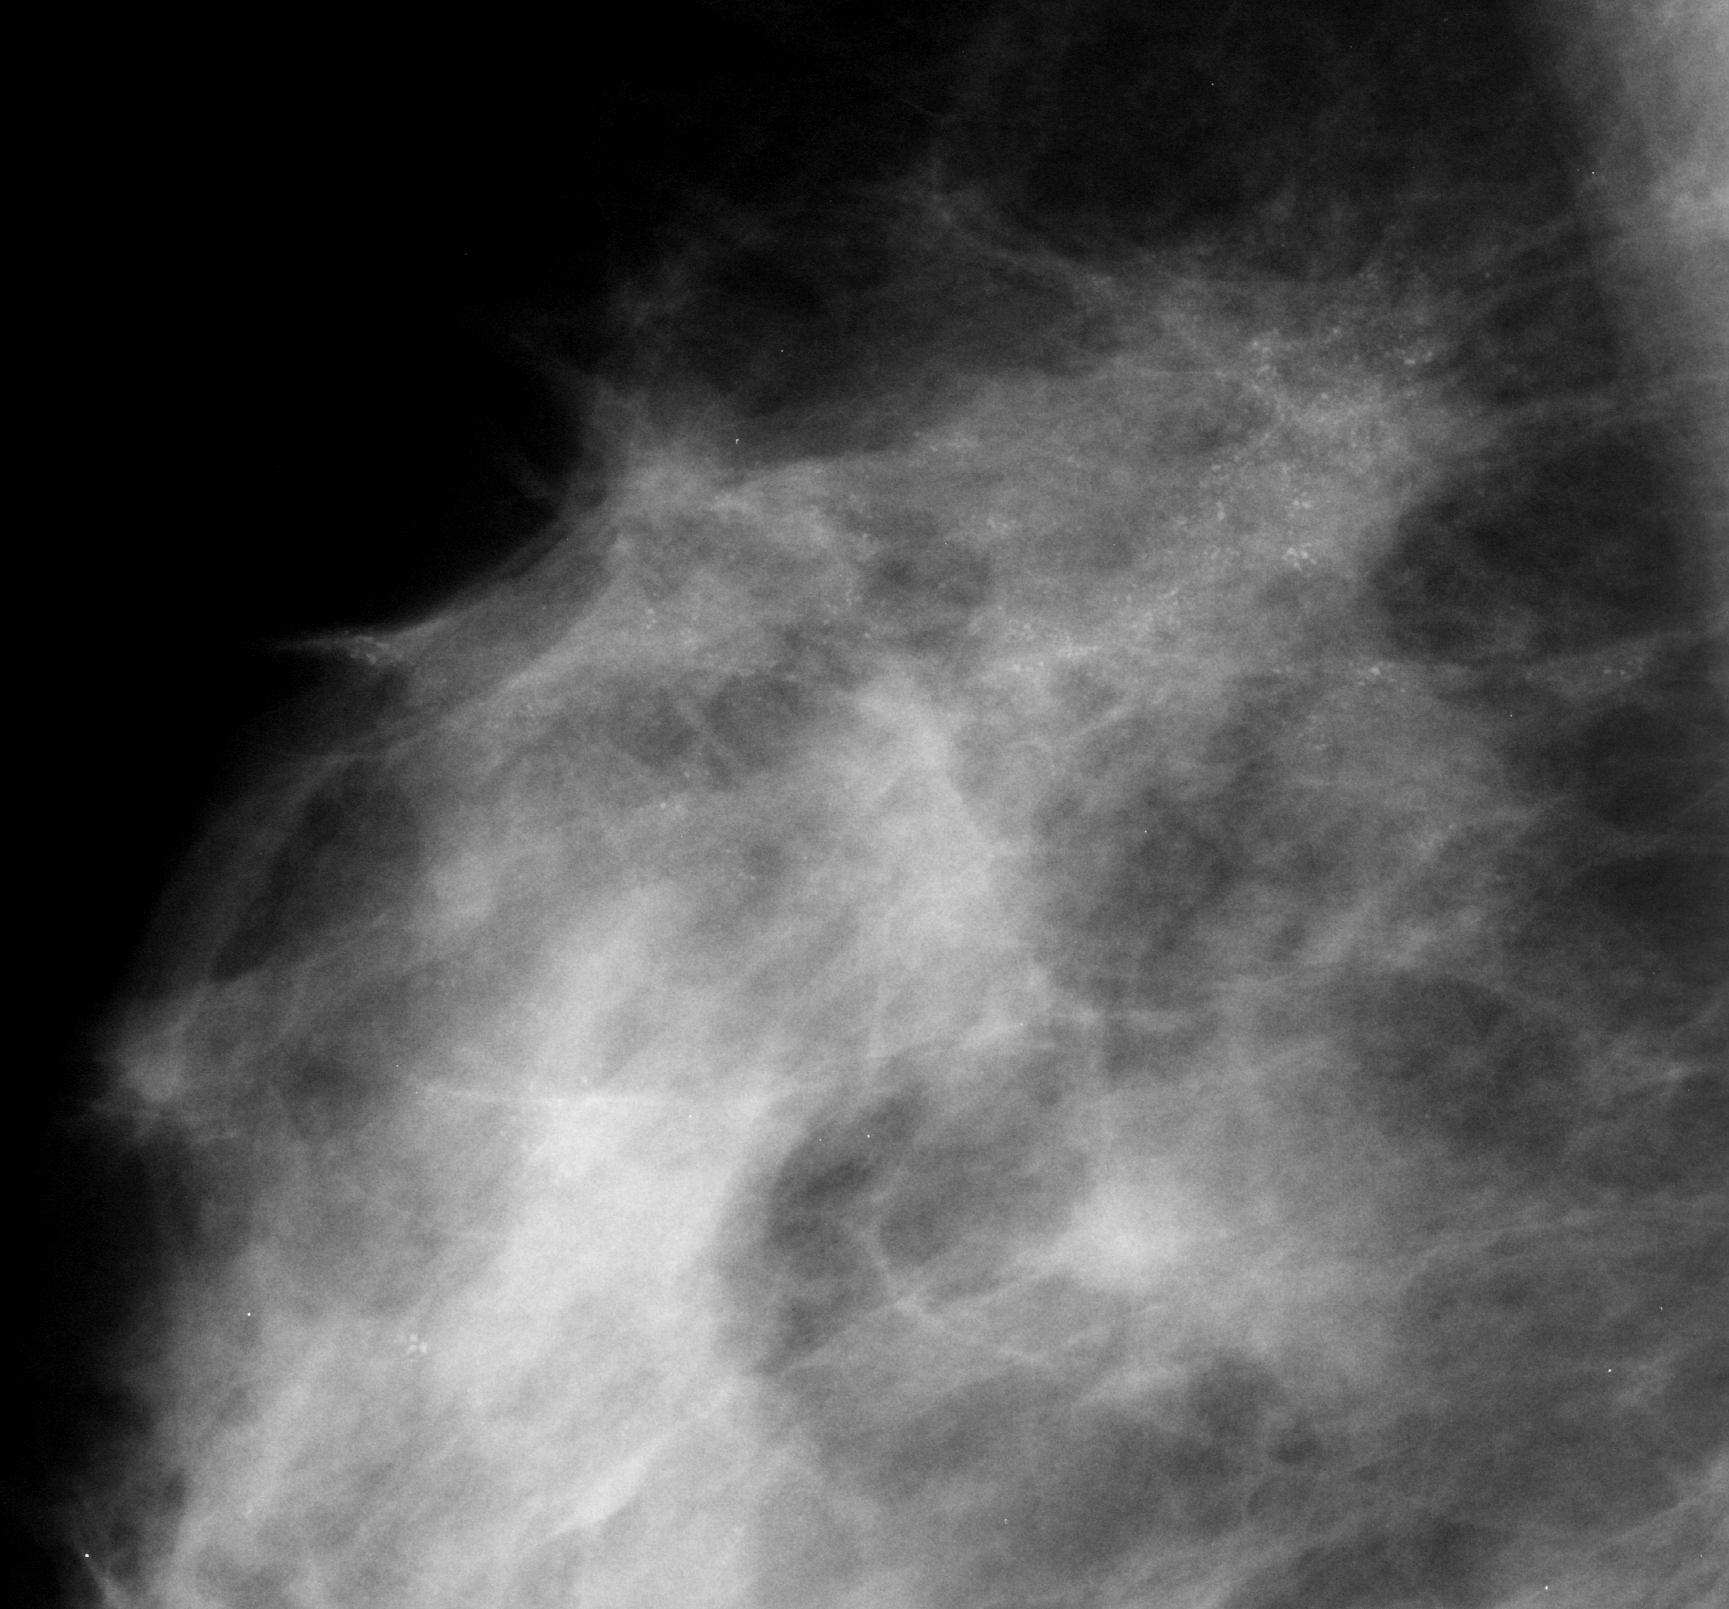
Cropped region of a digitized screen-film mammogram centred on a radiologist-marked abnormality, right breast, MLO view.
Finding: calcifications, morphology pleomorphic, distribution regional; BI-RADS assessment category 5; subtlety rating 5 on a 1 (subtle) to 5 (obvious) scale; pathology result (as recorded, not read from the image): malignant.